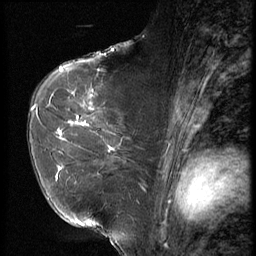
Breast MRI (dynamic contrast-enhanced), one sagittal slice; slice 39 of 56 in the series (ordered by position); 3 images stored at this slice position (order not interpretable as contrast timing); 1.5 T; TE 4.2 ms, TR 9 ms; 256 × 256 image matrix, field of view 180 × 180 mm. Patient: female, 61 years. Case-level facts recorded for this patient, not image findings: setting: breast cancer imaged before/during neoadjuvant chemotherapy; receptor status: HR-positive, HER2-negative.
Structures marked on this image (semi-automatic segmentation, software-assisted and operator-edited):
- analysis volume of interest (the breast-tissue region the enhancement analysis was run in; not a lesion): bounding box (x1, y1, x2, y2) in pixels: (47, 89, 153, 191)
- tumour enhancement mask (voxels above the 140 % enhancement threshold inside the analysis volume of interest): (52, 94, 113, 179)